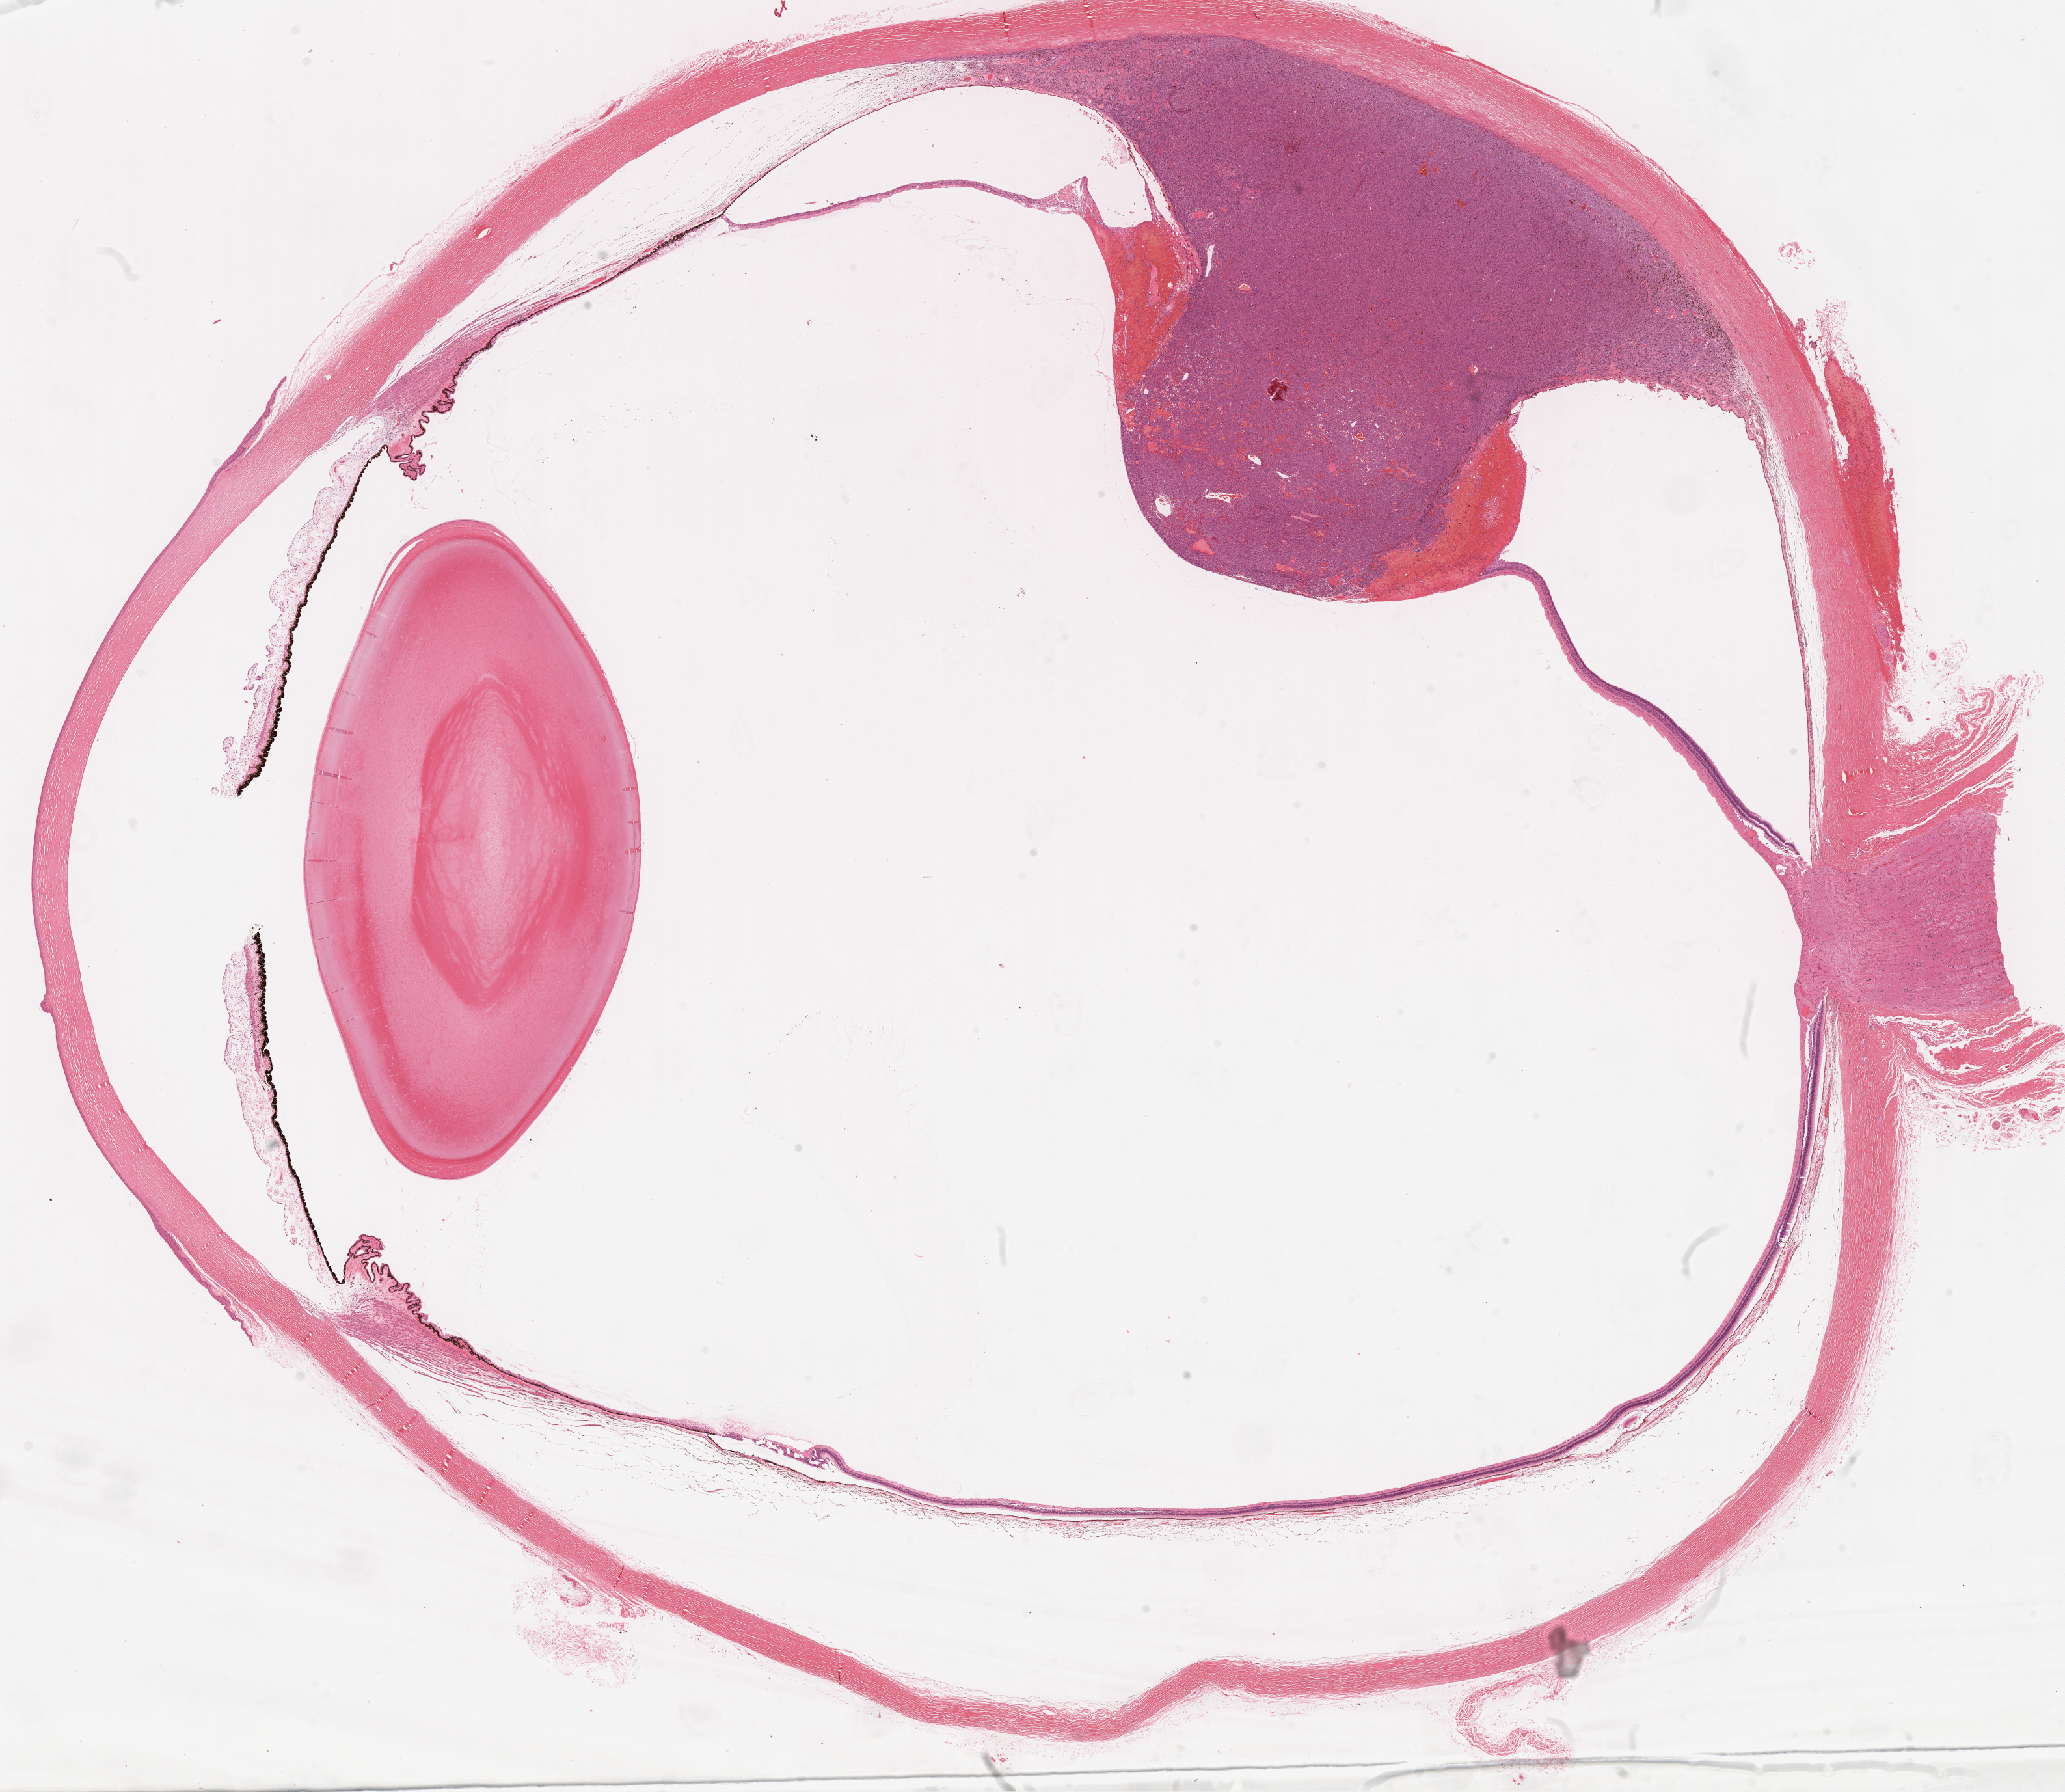
H&E-stained whole-slide image — whole scanned area (about 25.6 x 22.2 mm, from a 20x scan) shown as a low-resolution overview; formalin-fixed paraffin-embedded (FFPE) diagnostic section; uvea, primary tumour sample. Female, age 47 years at initial diagnosis.
Diagnosis: Spindle cell melanoma, type B (choroid).